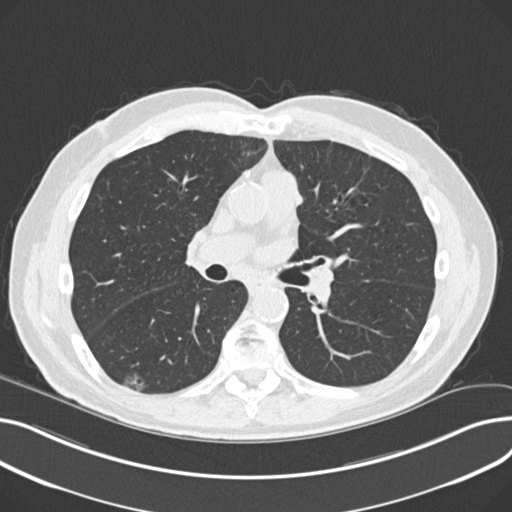
Chest CT (low-dose screening protocol), one axial image, third annual screen, lung window (W 1500 / L -600 HU), 2 mm slice thickness, standard (soft-tissue) reconstruction kernel (B30f). Male, age 68 years at enrolment. Current smoker at enrolment.
Expert reader's lesion annotation, bounding box <123,366,159,398> (left, top, right, bottom; pixels). The screening reader recorded 5 non-calcified nodules or masses ≥4 mm on this exam; which of them this box marks is not recorded. Official screen result: positive, other. Participant outcome: lung cancer diagnosed 247 days after this screen — non-small cell carcinoma, right lower lobe, poorly differentiated (G3), stage IA (AJCC 6th edition), 23 mm at pathology.